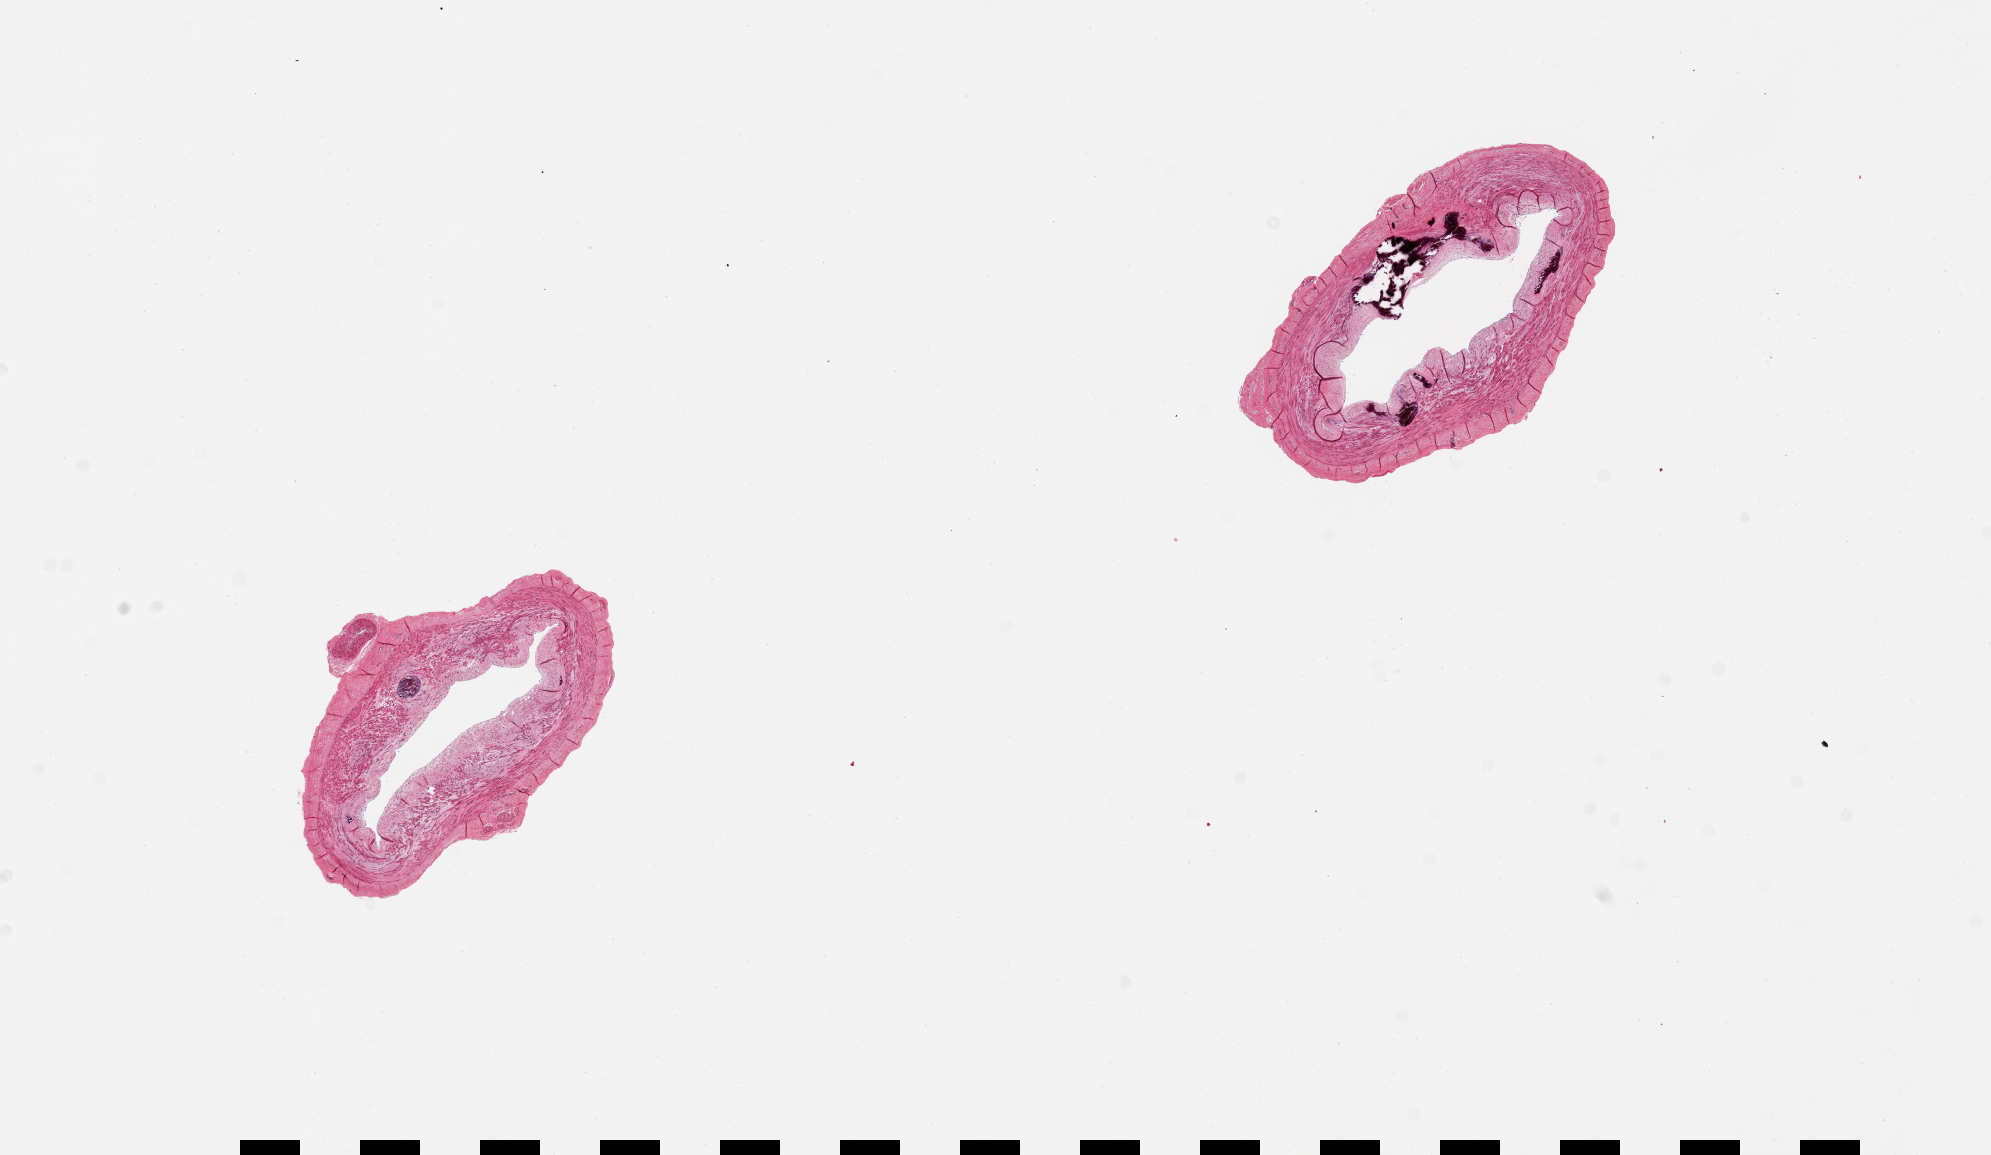
Digitized H&E-stained section — shown as a low-resolution overview of the whole scanned area (about 15.8 x 9.1 mm). PAXgene-fixed paraffin-embedded (PFPE) section. Sampled site (target tissue): tibial artery. Donor tissue sample. Donor sex: male.
* review note (as recorded): 2 pieces, 3x2 & 3x2mm; large calcified deposits in one, up to 1 cm; other piece has small calfied deposit